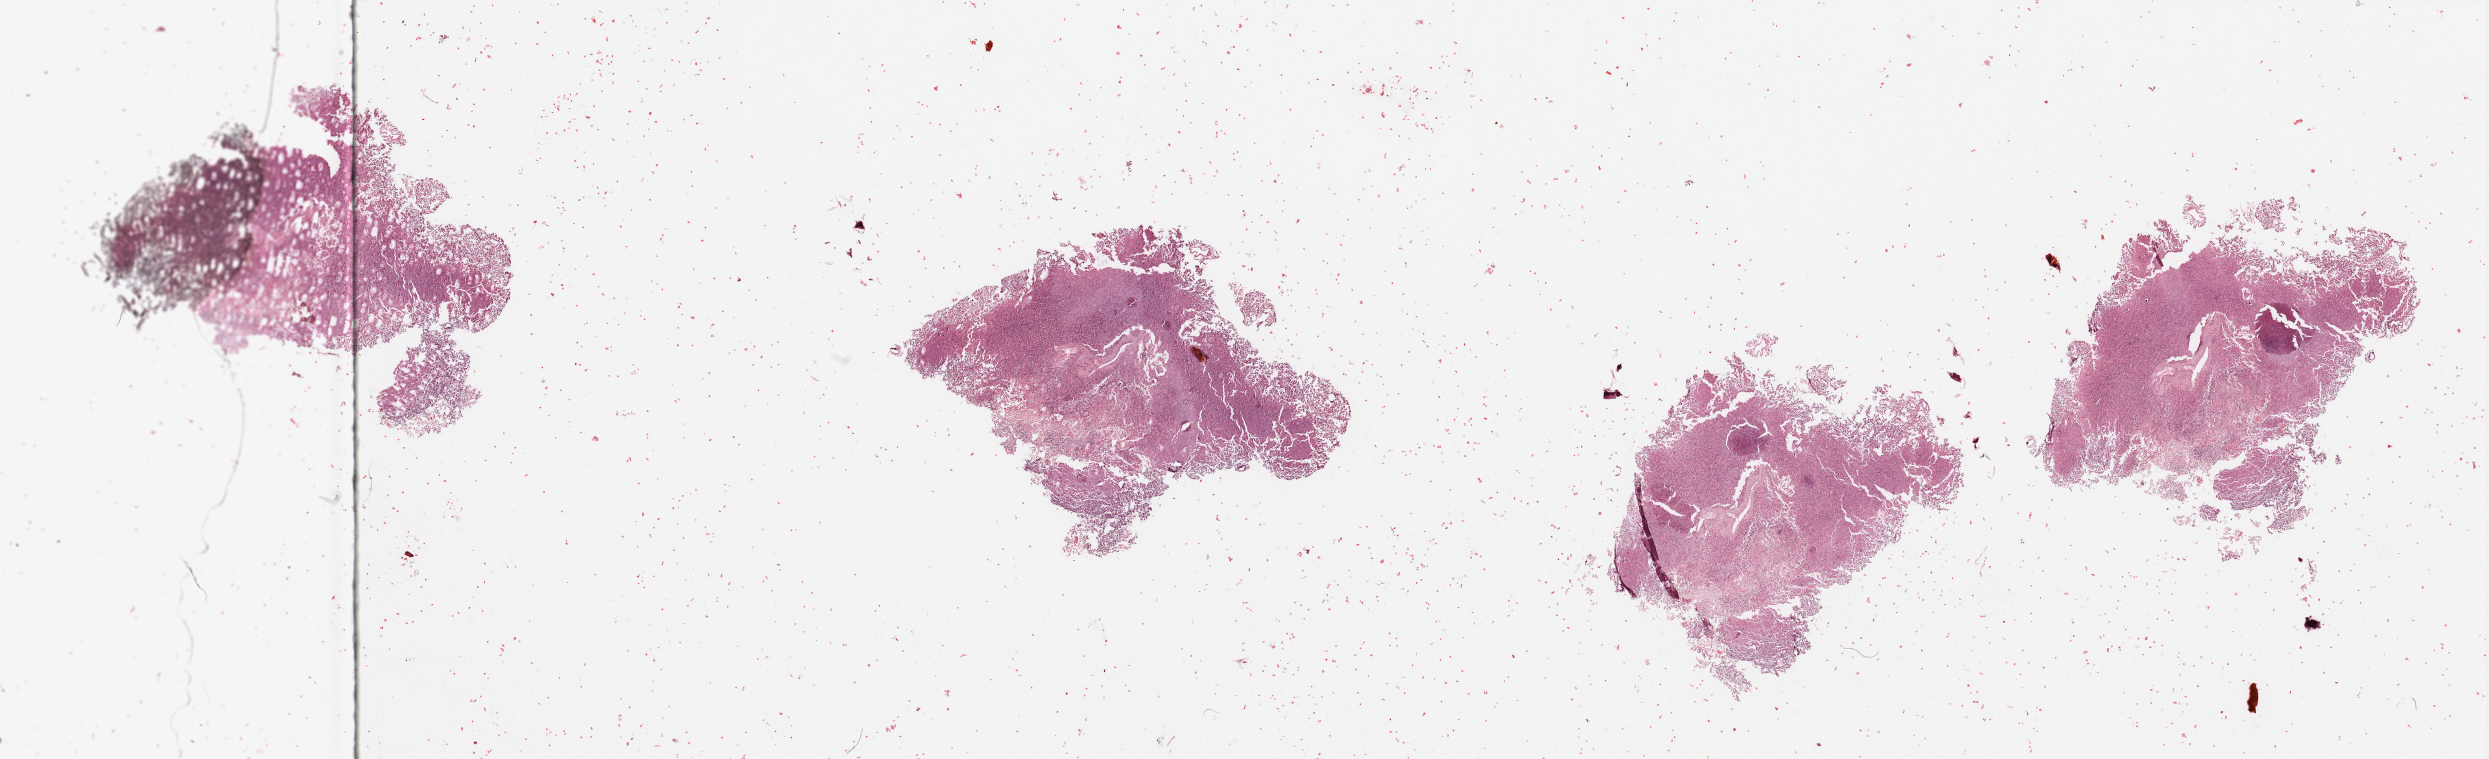
Digitized H&E-stained tissue section (whole slide) — a low-resolution overview of the entire scanned area, about 39.4 x 12.0 mm (acquisition: 20x scan), brain, tumour tissue. 34-year-old female patient.
Diagnosis: Glioblastoma.